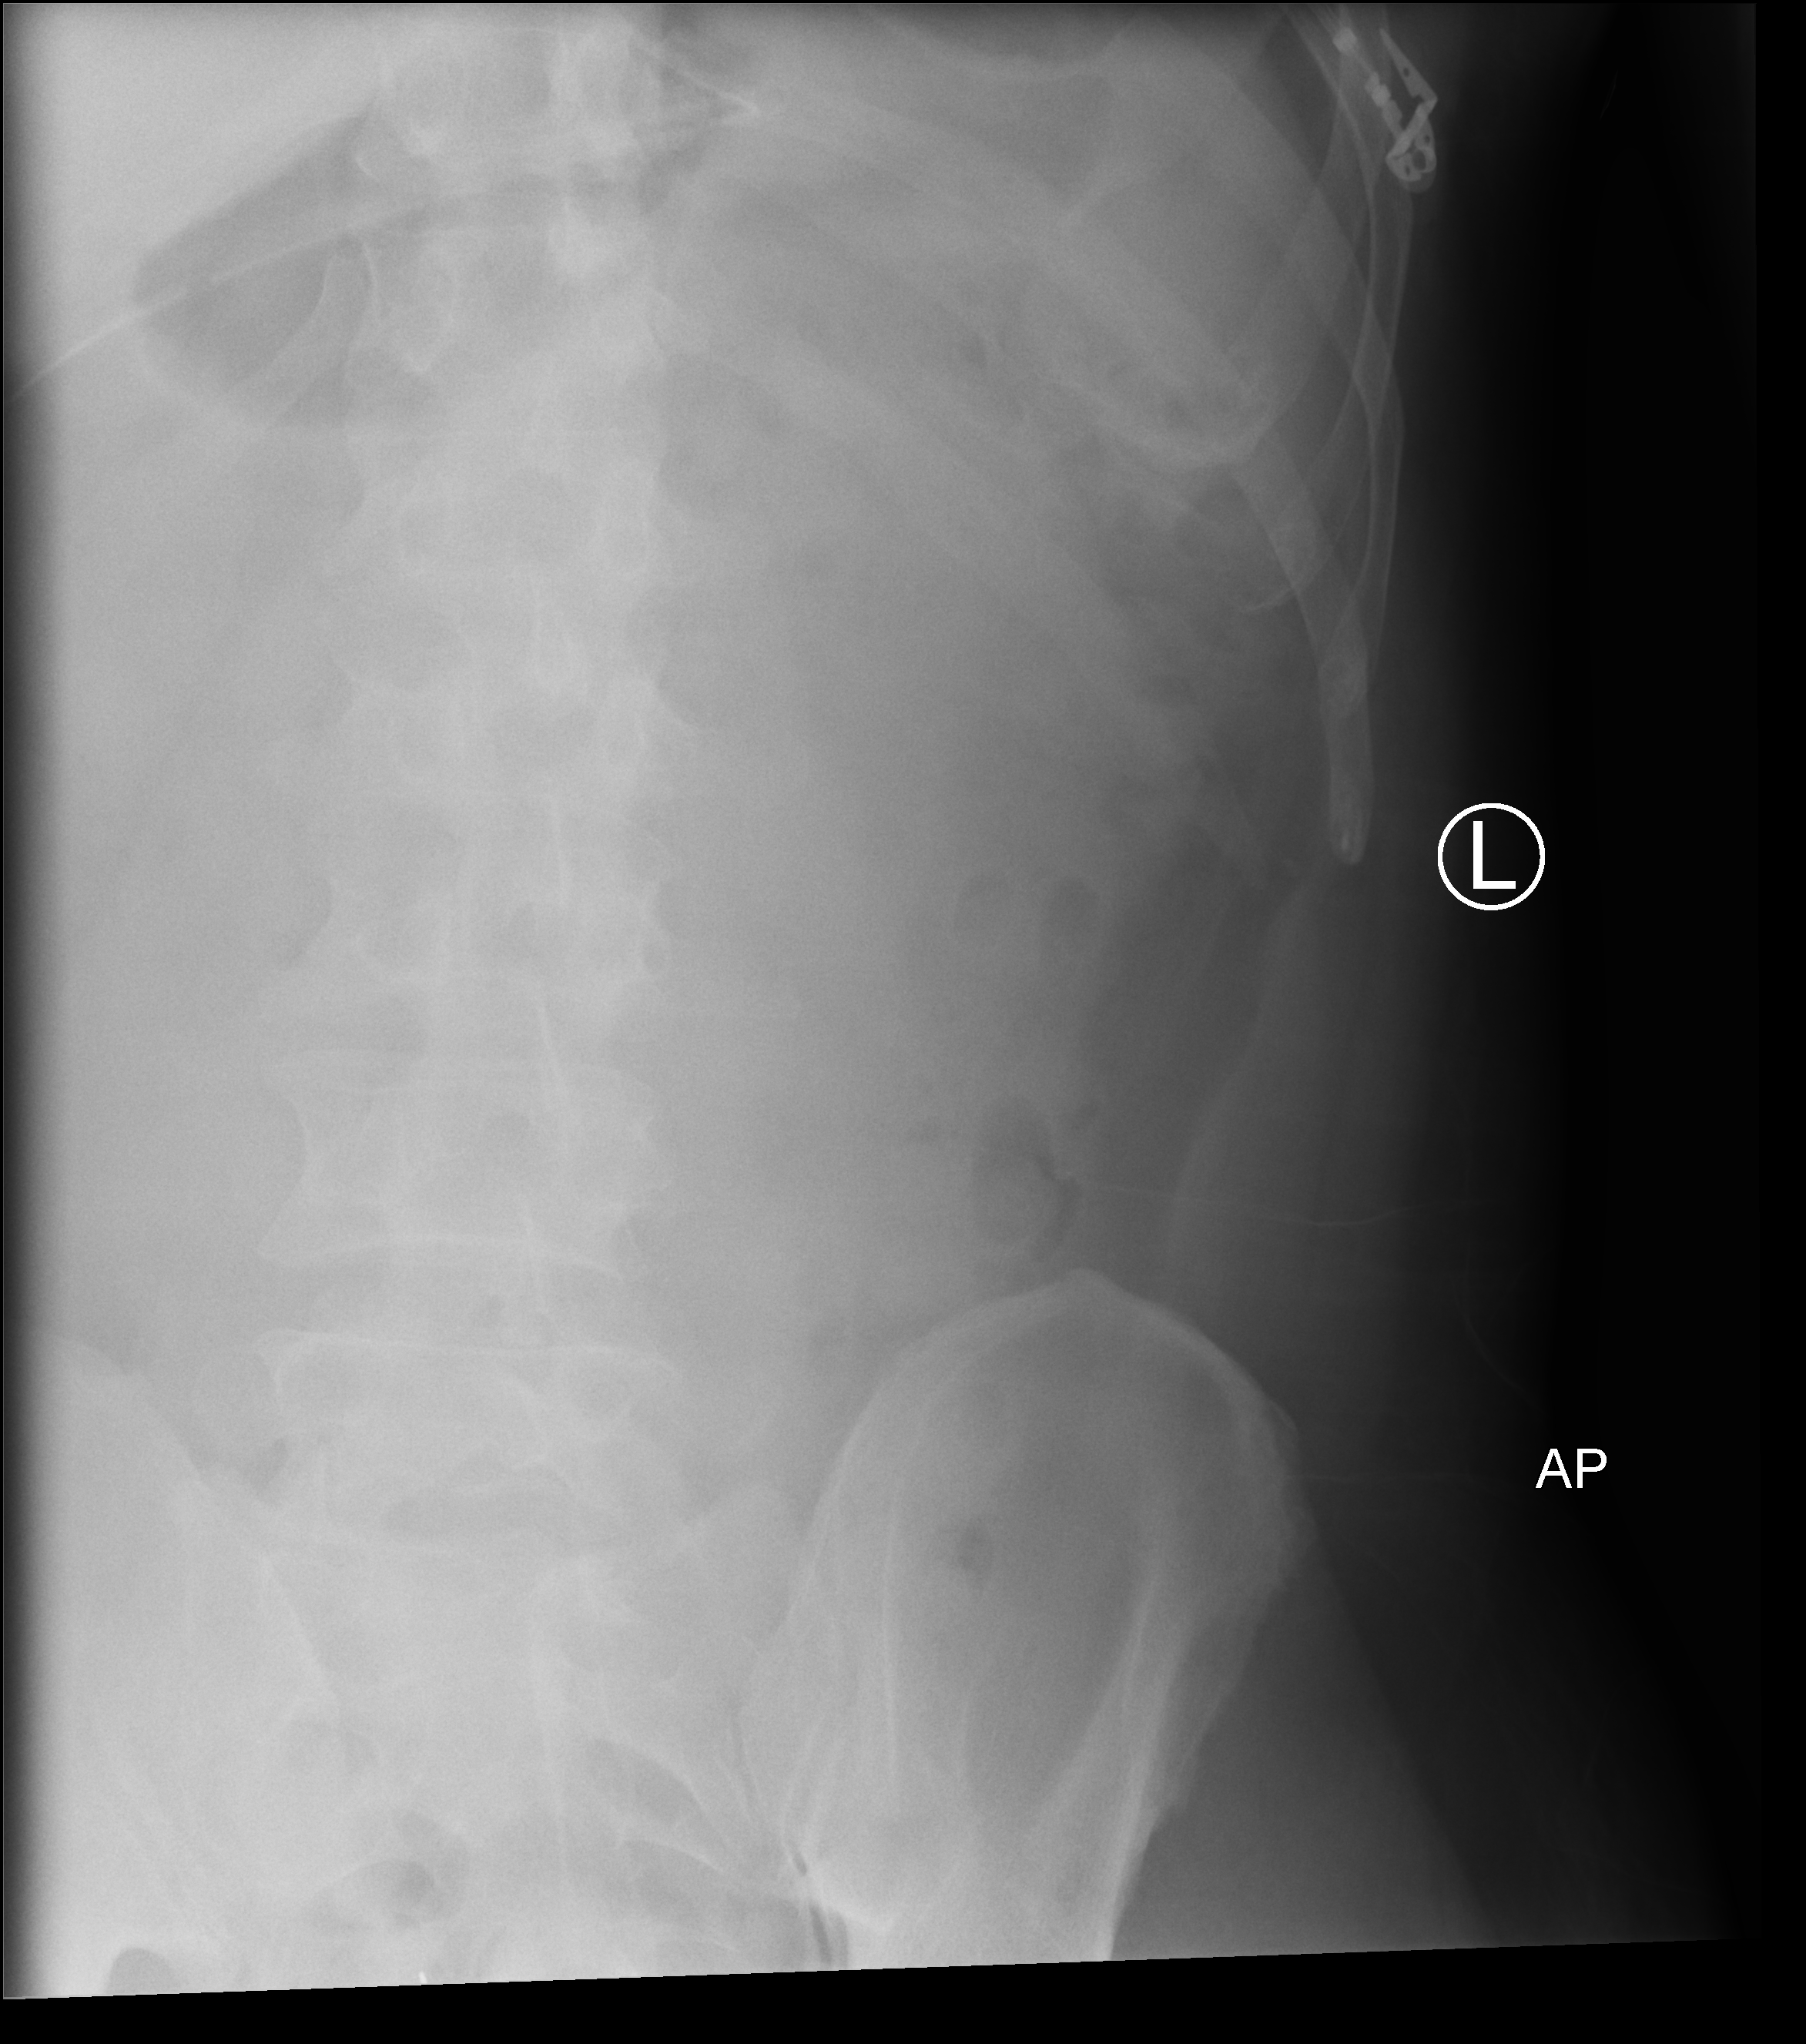
Bedside abdomen radiograph (computed radiography), anteroposterior (AP) projection. Patient hospitalised with COVID-19; male, aged 18–59 years.
Hospital-stay facts (about this admission, not read from this image; timing relative to this image not recorded): admitted to intensive care during this hospital stay: no.